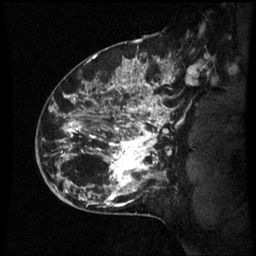
Breast MRI (dynamic contrast-enhanced), one sagittal slice; slice 46 of 60 in the series (ordered by position); dynamic contrast-enhanced series, image 2 of 3 at this slice position (ordered by acquisition); 1.5 T; TE 4.2 ms, TR 8.9 ms; 256 × 256 image matrix, field of view 200 × 200 mm. Patient: female, 42 years. From the clinical record (not read from this slice): setting: breast cancer imaged before/during neoadjuvant chemotherapy; receptor status: HER2-positive.
Outlined on this slice (semi-automatically segmented with operator editing):
- analysis volume of interest (the breast-tissue region the enhancement analysis was run in; not a lesion): bounding box <66,82,173,193> (left, top, right, bottom; pixels)
- tumour enhancement mask (voxels above the 70 % enhancement threshold inside the analysis volume of interest): <66,82,173,193>